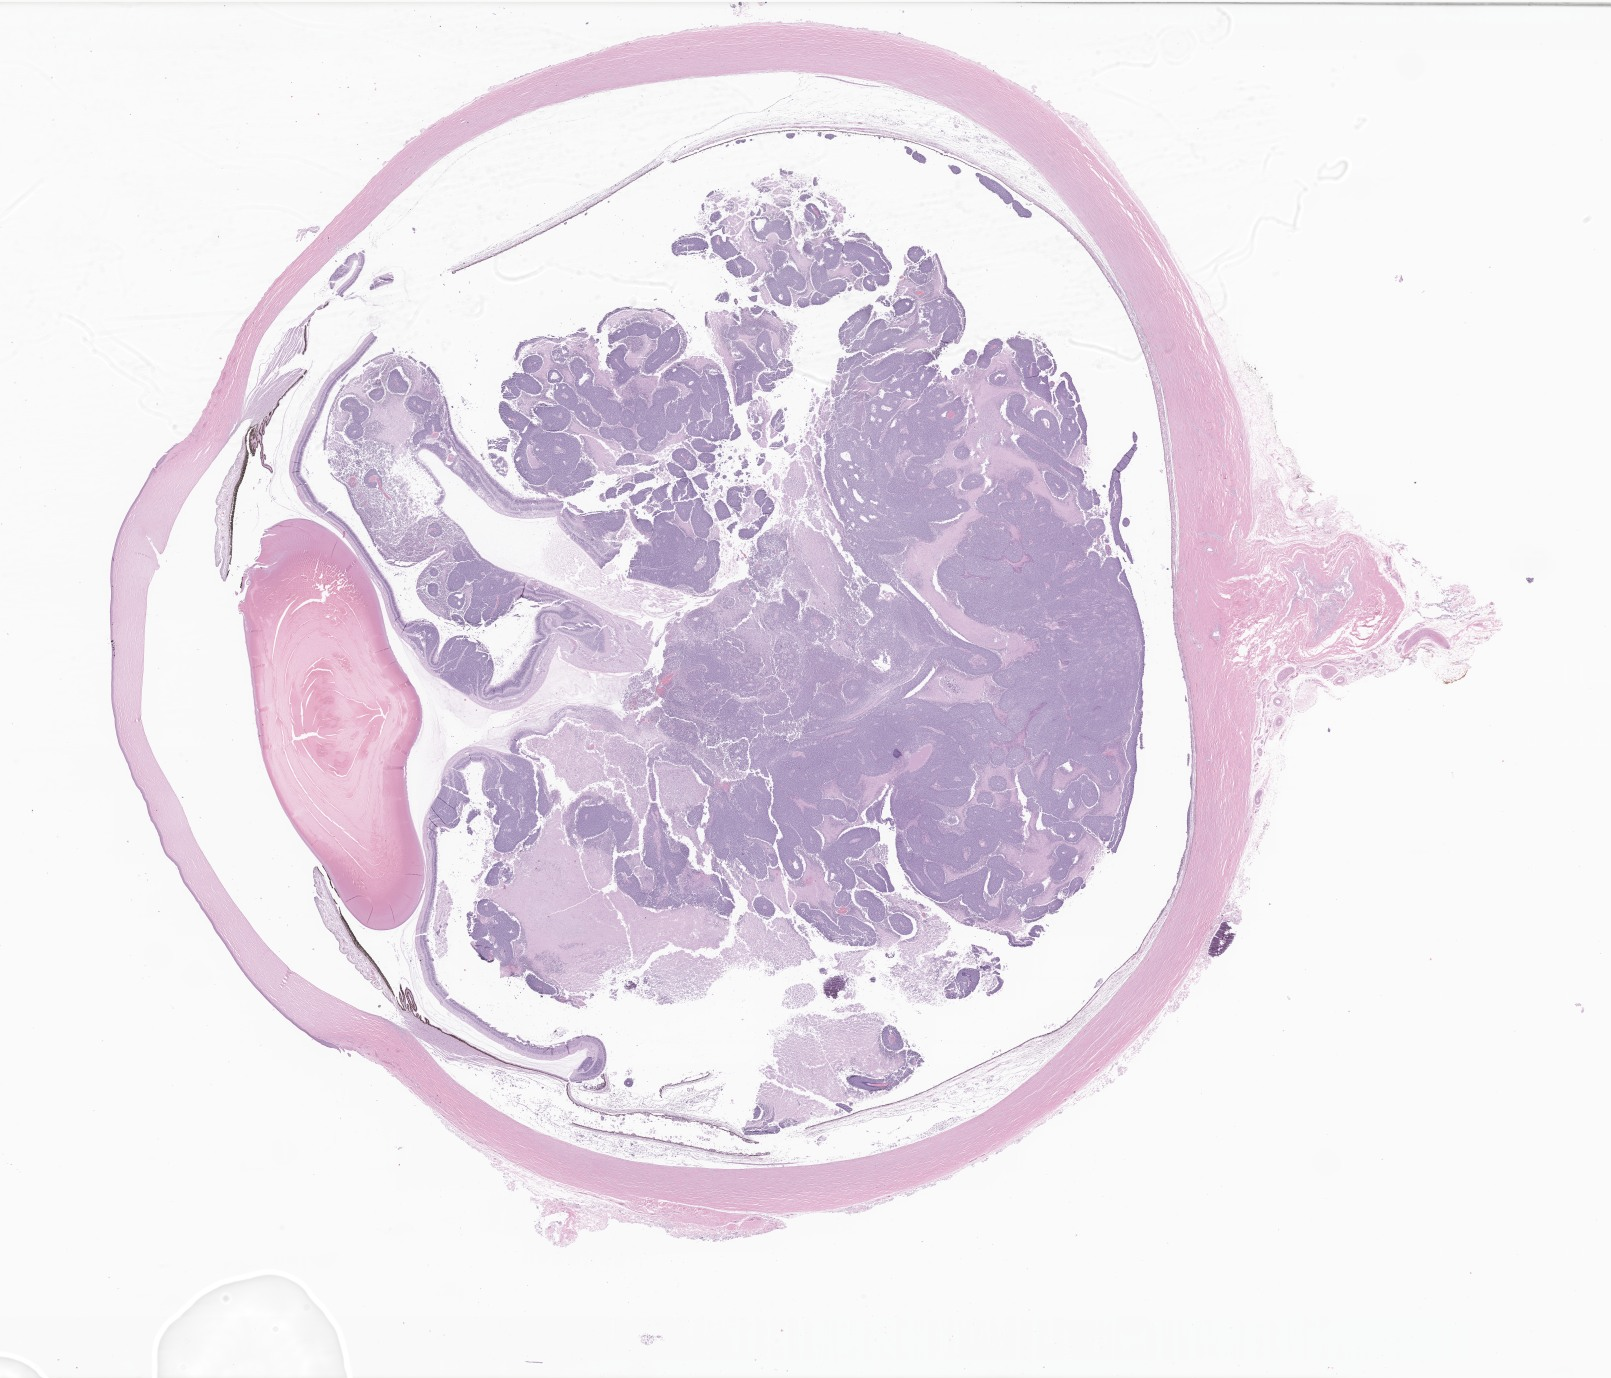
Whole-slide image, H&E stain of tumor tissue from the eye — a low-resolution overview of the entire scanned area, about 27.2 x 23.2 mm; formalin-fixed paraffin-embedded section. Patient: female, age 632 days (about 1.7 years).
- diagnosis (ICD-O-3 morphology term): Retinoblastoma, NOS